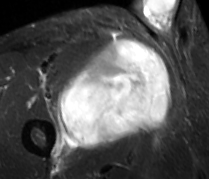
MRI of an extremity soft-tissue mass, one axial slice. Slice 53 of 89 in the series (ordered by position). STIR. MR volume resampled by the dataset authors to the PET/CT grid (not the native acquisition matrix). 209 × 179 image matrix, field of view 204 × 175 mm. Male patient. From the clinical record (not read from this slice): histological type: undifferentiated - pleiomorphic; grade: high; site of the primary tumour: right thigh.
Outlined on this slice (expert contour drawn on MRI and transferred to this co-registered scan by the dataset authors):
- gross tumour volume including surrounding oedema: box from (x=55, y=39) to (x=170, y=150) px
- gross tumour volume (mass): (x=59, y=39)–(x=170, y=149)